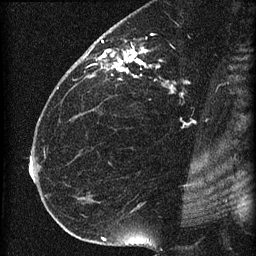
Breast MRI (dynamic contrast-enhanced), one sagittal slice; slice 39 of 60 in the series (ordered by position); dynamic contrast-enhanced series, image 2 of 4 at this slice position (ordered by acquisition); 1.5 T; TE 4.2 ms, TR 22.7 ms; 1.5 mm slice thickness; 256 × 256 image matrix, field of view 180 × 180 mm. Patient: female, 35 years. Case-level facts recorded for this patient, not image findings: setting: breast cancer imaged before/during neoadjuvant chemotherapy; receptor status: HR-positive, HER2-negative.
Structures marked on this image (semi-automatically segmented with operator editing):
- analysis volume of interest (the breast-tissue region the enhancement analysis was run in; not a lesion): bounding box (x1, y1, x2, y2) in pixels: (69, 27, 199, 112)
- tumour enhancement mask (voxels above the 90 % enhancement threshold inside the analysis volume of interest): (87, 40, 172, 88)